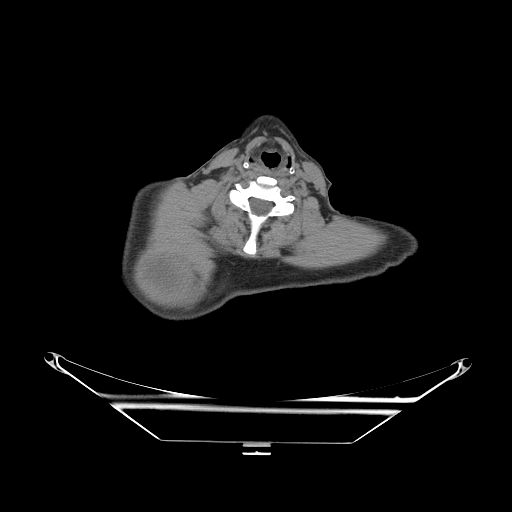
CT of an extremity soft-tissue mass (from a PET/CT study), one axial slice; slice 219 of 267 in the series (ordered by position); 140 kVp; soft-tissue window (W 400 / L 40 HU); 3.75 mm slice thickness; 512 × 512 image matrix, field of view 500 × 500 mm. Male patient. Case-level facts recorded for this patient, not image findings: histological type: pleiomorphic spindle cell undifferentiated; grade: high; site of the primary tumour: right parascapusular.
Structures marked on this image (expert contour drawn on MRI and transferred to this co-registered scan by the dataset authors):
- gross tumour volume including surrounding oedema: bounding box <135,260,209,303> (left, top, right, bottom; pixels)
- gross tumour volume (mass): <139,260,188,300>